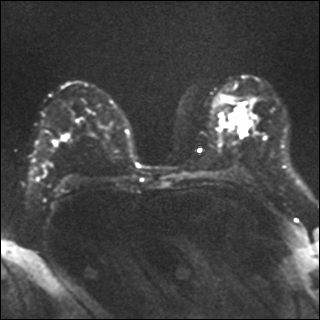
Breast MRI, one axial slice; position 22 of 40 along the scan axis; diffusion-weighted series; image 2 of 4 stored at this slice position (different b-values; order by instance number); 1.5 T; 320 × 320 image matrix, field of view 320 × 320 mm. Female patient.
Structures marked on this image (manually delineated by an expert):
- tumour on diffusion-weighted imaging: bounding box (x1, y1, x2, y2) in pixels: (237, 108, 251, 136)